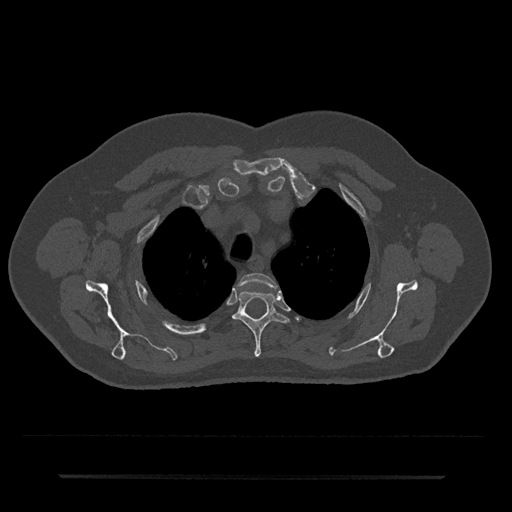
CT including the spine, one axial slice; slice 570 of 797 in the series (ordered by position); reconstruction kernel Br40s/3; 120 kVp; bone window (W 1800 / L 400 HU); 0.5 mm slice thickness; 512 × 512 image matrix. Patient: male, 69 years. From the clinical record (not read from this slice): primary cancer: prostate.
Outlined on this slice (semi-automatic segmentation, software-assisted and operator-edited):
- T2 vertebra: bounding box (x1, y1, x2, y2) in pixels: (238, 273, 277, 288)
- T3 vertebra: (233, 290, 288, 357)